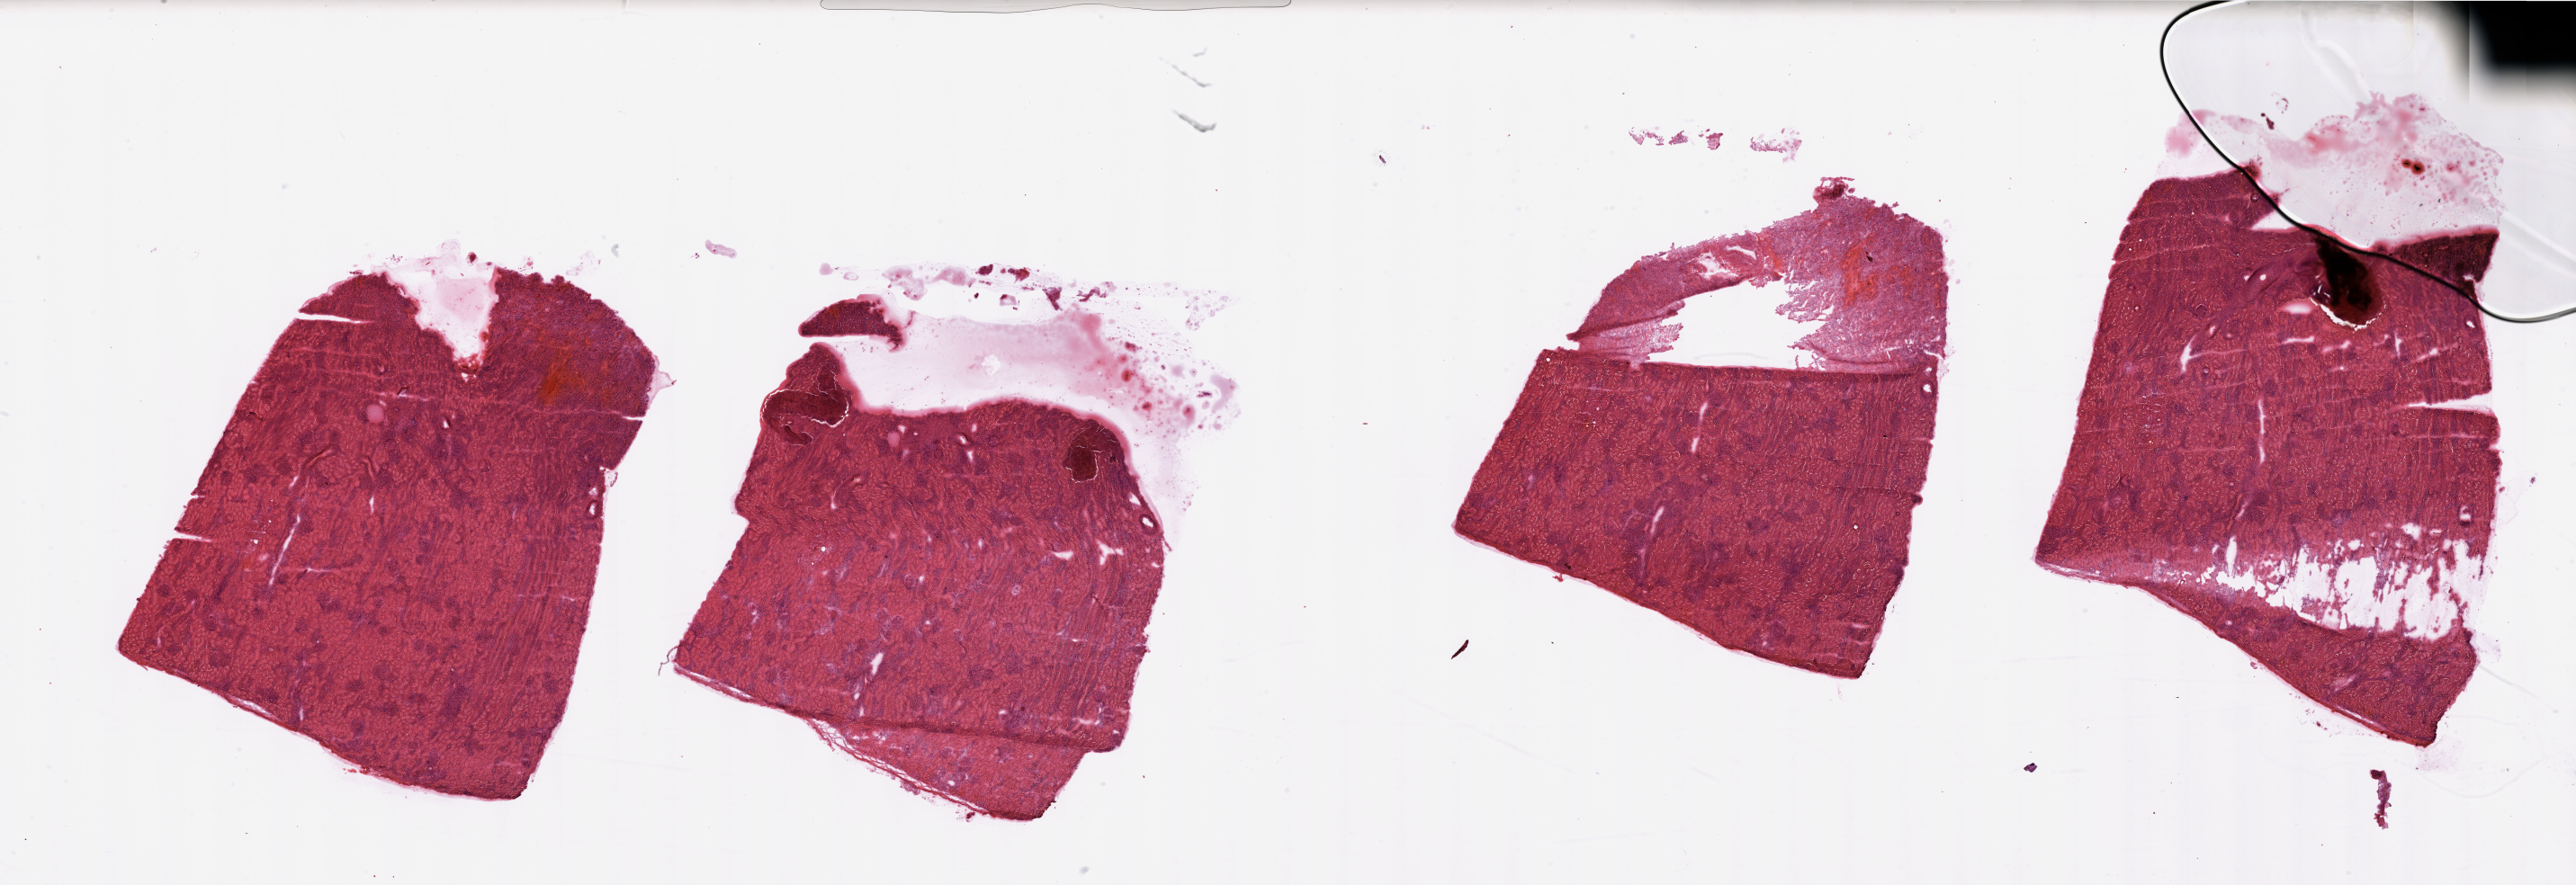
Whole-slide histology image, Hematoxylin and eosin (H&E) stained, whole scanned area (about 45.3 x 15.6 mm) shown as a low-resolution overview, normal (non-tumour) tissue sample, sampled site: kidney. Male, 68 y/o.
This section: normal (non-tumour) tissue from the same patient. Patient diagnosis: Renal cell carcinoma, NOS.